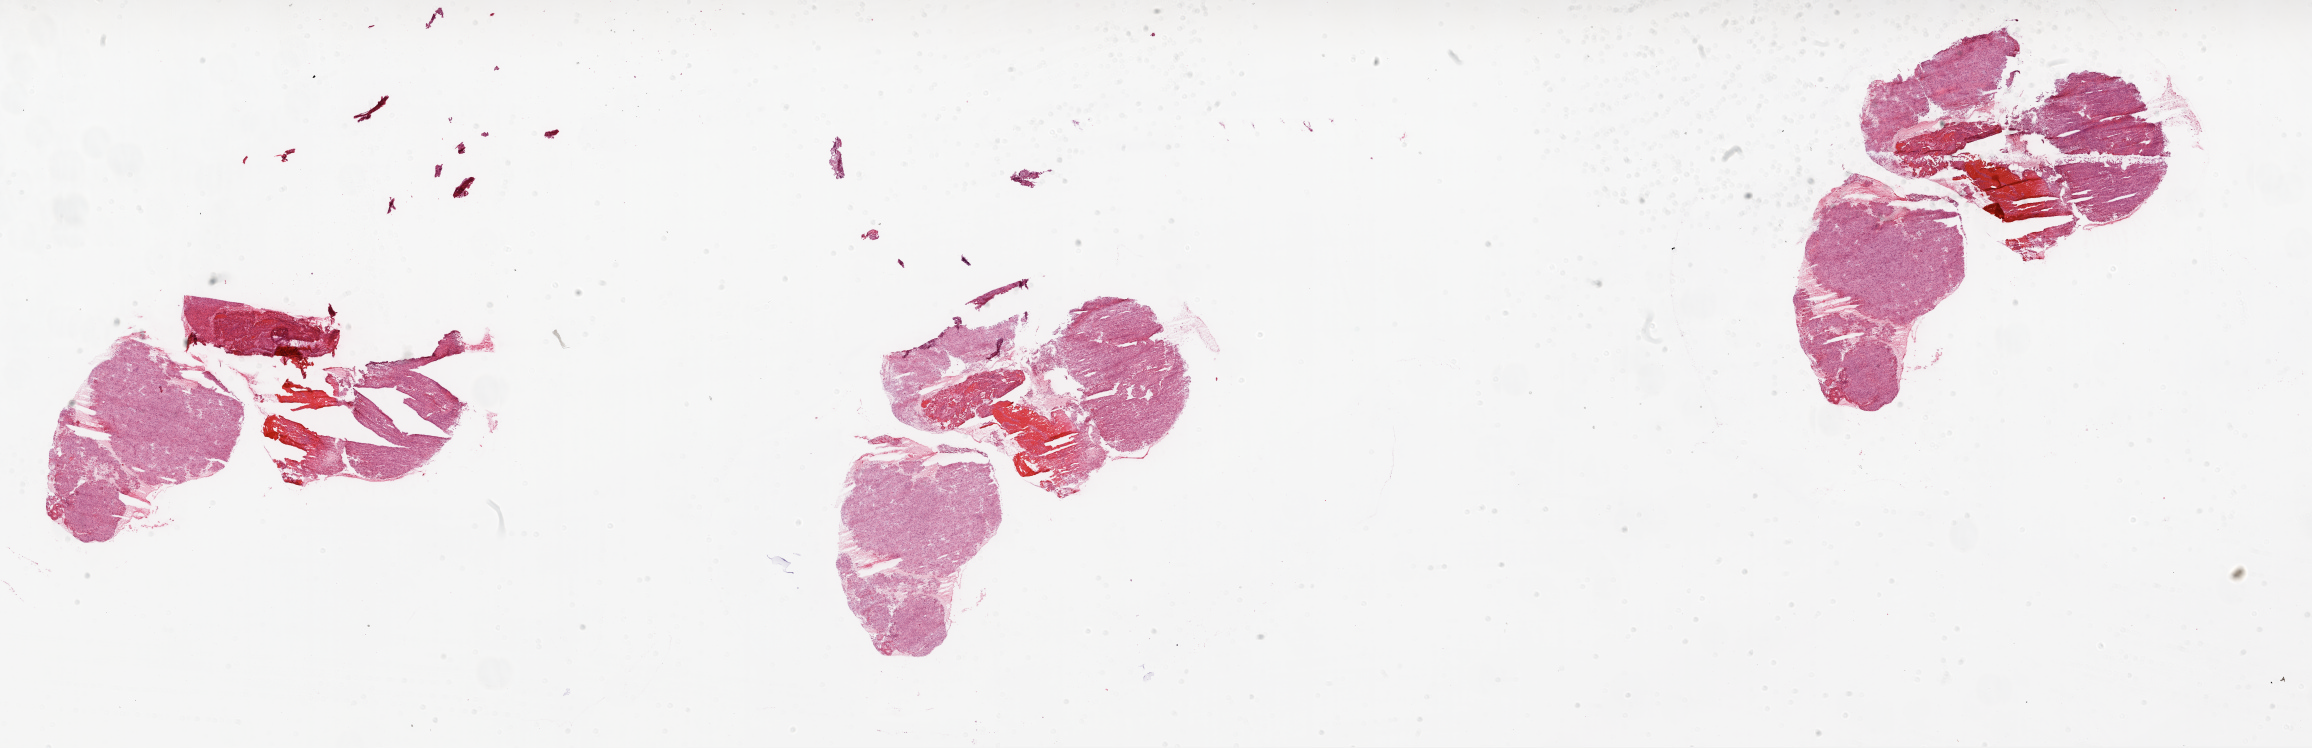
Digitized H&E tissue section (whole slide), whole scanned area (about 37.1 x 12.0 mm, from a 20x scan) shown as a low-resolution overview, frozen section from the top of the tissue portion, brain, primary tumour sample. Female, age 59 years at initial diagnosis. Composition of this section per pathologist review: tumour cells 75%, tumour nuclei 85%, normal cells 0%, stromal cells 10%, necrosis 15%.
Pathologic diagnosis: Glioblastoma.